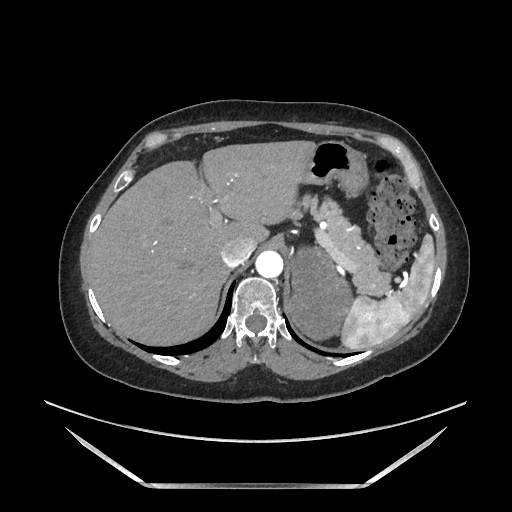
Contrast-enhanced abdominal CT, one axial slice; position 138 of 205 along the scan axis; soft-tissue window (W 400 / L 40 HU); 1.25 mm slice thickness; 512 × 512 image matrix, field of view 440 × 440 mm. Female patient. Case-level facts recorded for this patient, not image findings: diagnosis: adrenocortical carcinoma; tumour side: left adrenal; tumour size at pathology: 12.5 cm; Ki-67 index: 39 %; stage (as recorded): 3.
Outlined on this slice (semi-automatic segmentation, software-assisted and operator-edited):
- mass: bounding box <291,251,351,339> (left, top, right, bottom; pixels)